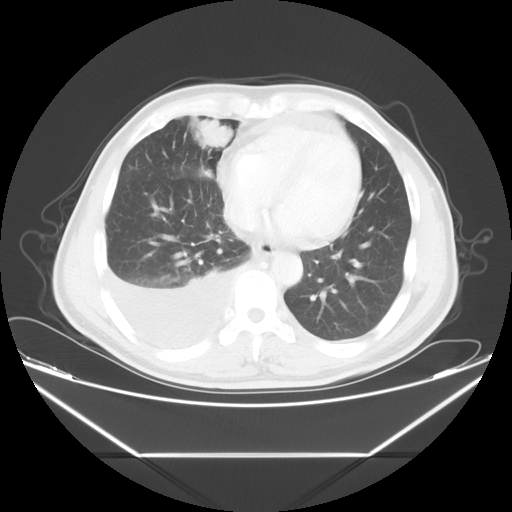
Chest CT, one axial slice. Slice 19 of 56 in the series (ordered by position). Reconstruction kernel STANDARD. Lung window (W 1500 / L -600 HU). 5 mm slice thickness. 512 × 512 image matrix, field of view 412 × 412 mm. Male patient, age 57 years. From the clinical record (not read from this slice): clinical TNM (as recorded): T2 N3 M1.
Outlined on this slice (bounding box drawn by a radiologist):
- lung tumour (recorded histology: adenocarcinoma): bounding box <196,116,232,150> (left, top, right, bottom; pixels)